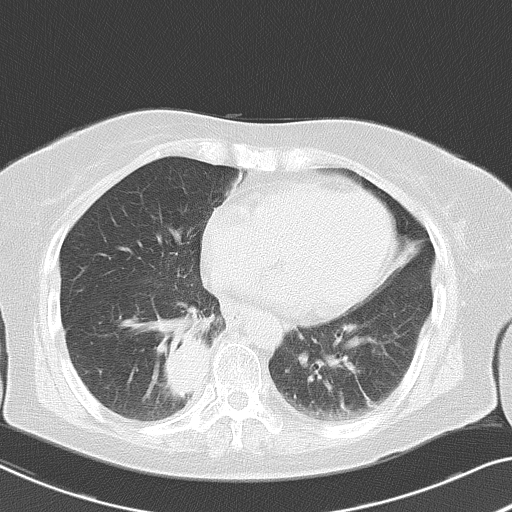
Chest CT, one axial slice. Slice 19 of 53 in the series (ordered by position). 120 kVp. Lung window (W 1500 / L -600 HU). 5 mm slice thickness. 512 × 512 image matrix. Female patient, age 70 years. Case-level facts recorded for this patient, not image findings: clinical TNM (as recorded): T2 N1 M1a.
Structures marked on this image (rectangle marked by the reading radiologist):
- lung tumour (recorded histology: adenocarcinoma): bounding box [x1, y1, x2, y2] px = [163, 330, 211, 406]